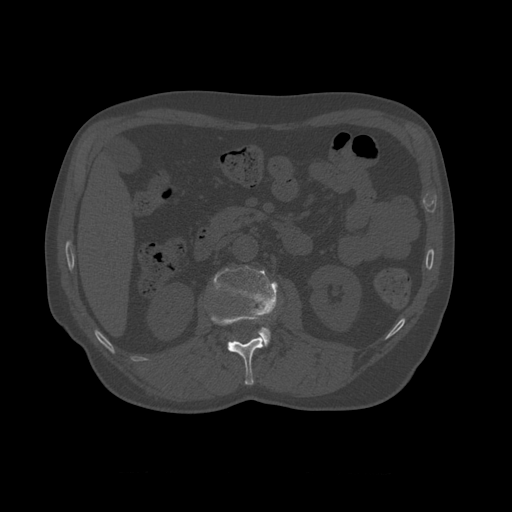
CT including the spine, one axial slice; slice 346 of 450 in the series (ordered by position); reconstruction kernel STANDARD; 120 kVp; bone window (W 1800 / L 400 HU); 1.25 mm slice thickness; 512 × 512 image matrix, field of view 405 × 405 mm. Patient age 75 years. Case-level facts recorded for this patient, not image findings: primary cancer: prostate.
Annotated regions visible in this slice (semi-automatic segmentation, software-assisted and operator-edited):
- L1 vertebra: bounding box (x1, y1, x2, y2) in pixels: (211, 314, 266, 385)
- L2 vertebra: (213, 266, 278, 347)